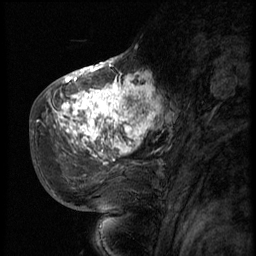
Breast MRI (dynamic contrast-enhanced), one sagittal slice; position 25 of 56 along the scan axis; 3 images stored at this slice position (order not interpretable as contrast timing); 1.5 T; TE 4.2 ms, TR 9 ms; 2.5 mm slice thickness; 256 × 256 image matrix, field of view 180 × 180 mm. Patient: female, 51 years. From the clinical record (not read from this slice): setting: breast cancer imaged before/during neoadjuvant chemotherapy; receptor status: triple-negative.
Structures marked on this image (semi-automatically segmented with operator editing):
- analysis volume of interest (the breast-tissue region the enhancement analysis was run in; not a lesion): bounding box (x1, y1, x2, y2) in pixels: (52, 66, 164, 179)
- tumour enhancement mask (voxels above the 140 % enhancement threshold inside the analysis volume of interest): (52, 66, 161, 165)